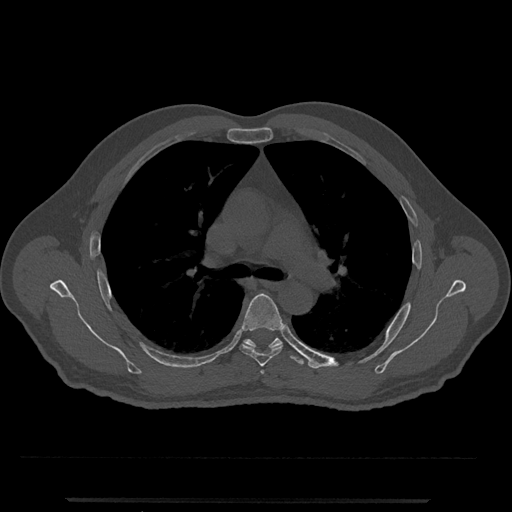
CT including the spine, one axial slice. Position 776 of 797 along the scan axis. Reconstruction kernel Br40s/3. Bone window (W 1800 / L 400 HU). 0.5 mm slice thickness. 512 × 512 image matrix, field of view 419 × 419 mm. Patient: male, 63 years. Case-level facts recorded for this patient, not image findings: primary cancer: prostate.
Structures marked on this image (semi-automatically segmented with operator editing):
- T5 vertebra: box from (x=239, y=293) to (x=283, y=367) px
- T6 vertebra: (x=243, y=337)–(x=304, y=366)